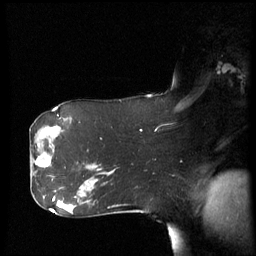
Breast MRI (dynamic contrast-enhanced), one sagittal slice; position 38 of 60 along the scan axis; dynamic contrast-enhanced series, image 2 of 3 at this slice position (ordered by acquisition); 1.5 T; TE 4.2 ms, TR 8.4 ms; 2.9 mm slice thickness; 256 × 256 image matrix, field of view 280 × 280 mm. Patient: female, 61 years. Case-level facts recorded for this patient, not image findings: setting: breast cancer imaged before/during neoadjuvant chemotherapy; receptor status: HR-positive, HER2-negative.
Annotated regions visible in this slice (semi-automatically segmented with operator editing):
- analysis volume of interest (the breast-tissue region the enhancement analysis was run in; not a lesion): bounding box <32,142,55,177> (left, top, right, bottom; pixels)
- tumour enhancement mask (voxels above the 70 % enhancement threshold inside the analysis volume of interest): <37,158,51,167>